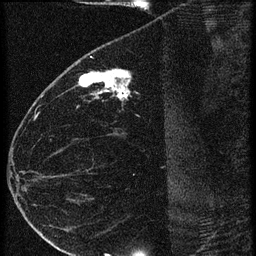
Breast MRI (dynamic contrast-enhanced), one sagittal slice. Position 27 of 60 along the scan axis. 3 images stored at this slice position (order not interpretable as contrast timing). 1.5 T. TE 4.2 ms, TR 20.4 ms. 1.5 mm slice thickness. 256 × 256 image matrix, field of view 180 × 180 mm. Female patient, age 35 years. From the clinical record (not read from this slice): setting: breast cancer imaged before/during neoadjuvant chemotherapy; receptor status: HR-positive, HER2-negative.
Annotated regions visible in this slice (semi-automatically segmented with operator editing):
- analysis volume of interest (the breast-tissue region the enhancement analysis was run in; not a lesion): bounding box (x1, y1, x2, y2) in pixels: (65, 60, 169, 119)
- tumour enhancement mask (voxels above the 90 % enhancement threshold inside the analysis volume of interest): (78, 70, 131, 101)